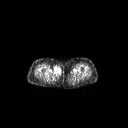
FDG PET of an extremity soft-tissue mass (from a PET/CT study), one axial slice; position 235 of 311 along the scan axis; 128 × 128 image matrix. Patient: female, 78 years. From the clinical record (not read from this slice): histological type: leiomyosarcoma; grade: intermediate; site of the primary tumour: parascapusular.
Structures marked on this image (expert contour drawn on MRI and transferred to this co-registered scan by the dataset authors):
- gross tumour volume including surrounding oedema: bounding box [x1, y1, x2, y2] px = [53, 65, 62, 76]
- gross tumour volume (mass): [53, 65, 62, 76]